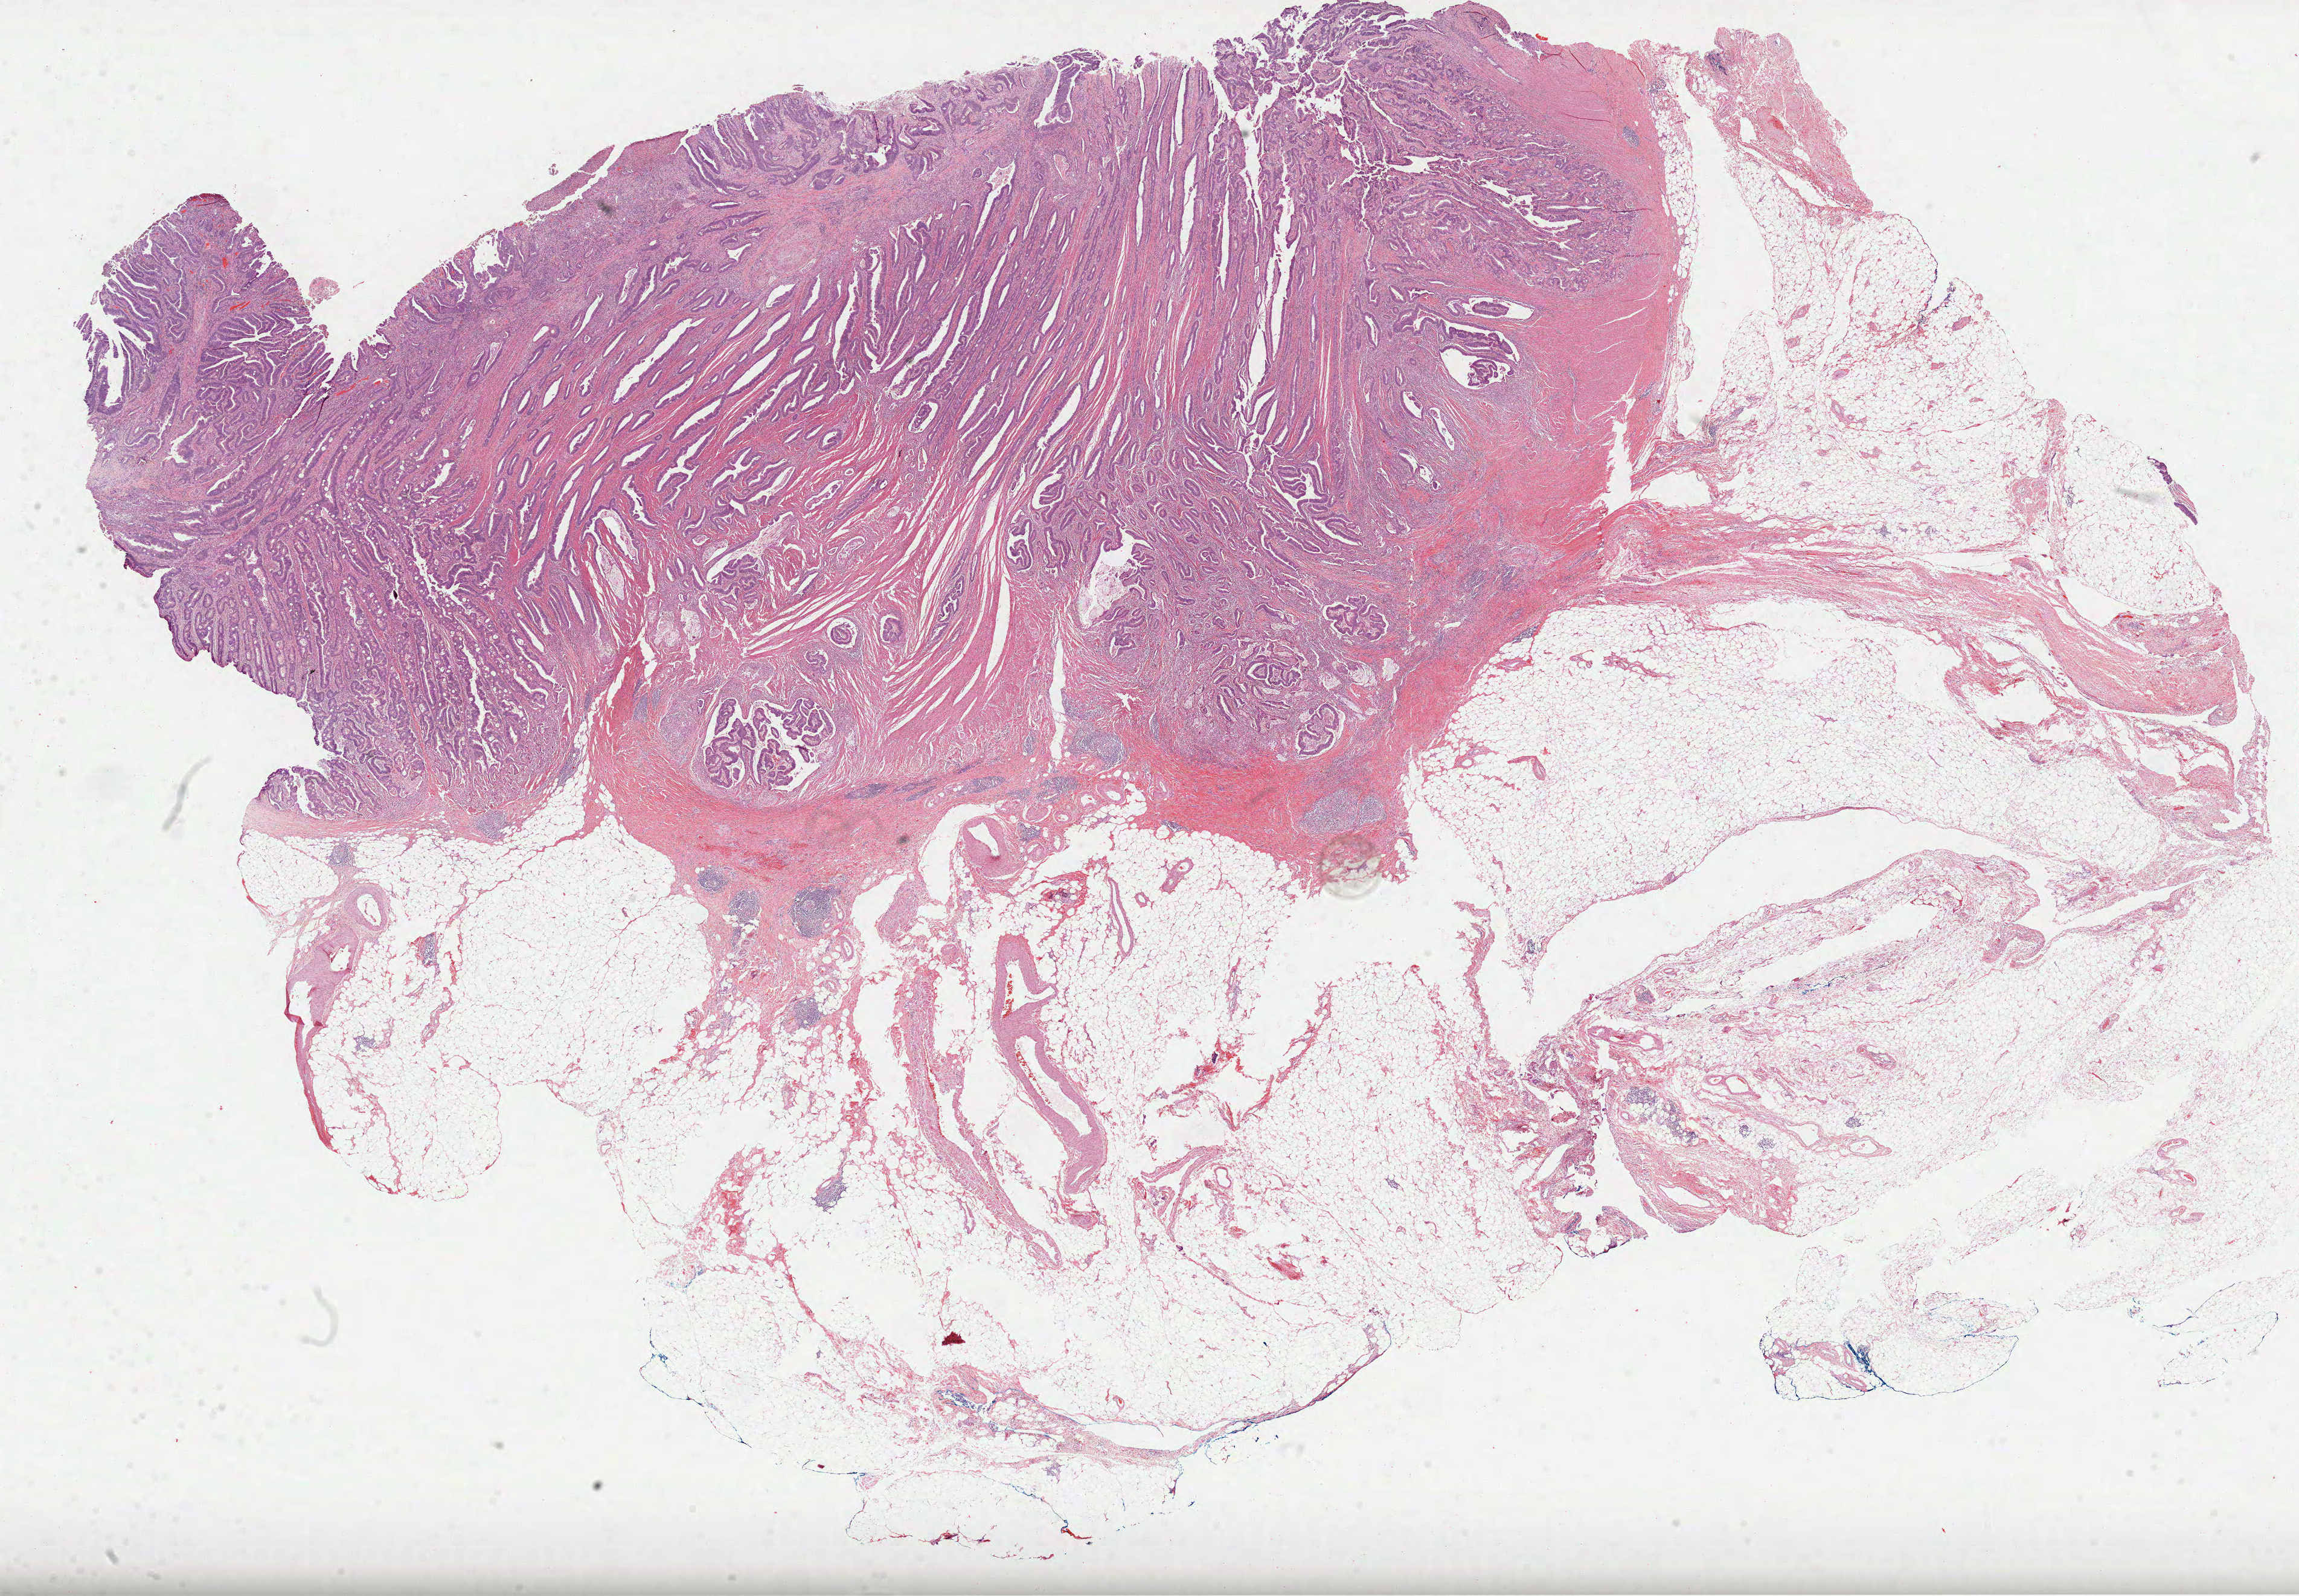
Digitized Hematoxylin and eosin (H&E) stained tissue section (whole slide), a low-resolution overview of the entire scanned area, about 30.7 x 21.3 mm (from a 40x scan). Formalin-fixed paraffin-embedded (FFPE) diagnostic section. Primary tumour sample from the colon. Patient sex: male.
Pathologic diagnosis: Adenocarcinoma, NOS (ascending colon).